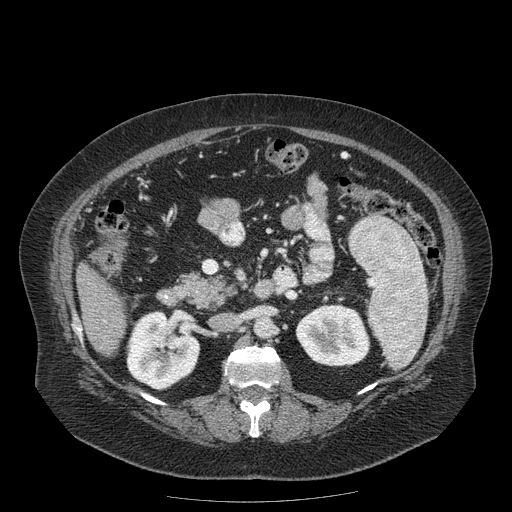
Contrast-enhanced abdominal CT (liver protocol), one axial slice. Slice 61 of 204 in the series (ordered by position). Reconstruction kernel STANDARD. 120 kVp. Soft-tissue window (W 400 / L 40 HU). 2.5 mm slice thickness. 512 × 512 image matrix, field of view 440 × 440 mm. Case-level facts recorded for this patient, not image findings: diagnosis: hepatocellular carcinoma (patient treated with transarterial chemoembolisation; whether this scan precedes or follows treatment is not stated here); TNM stage (as recorded): Stage-IIIB; Child-Pugh class: A; tumour differentiation: well differentiated; tumour nodularity: uninodular.
Structures marked on this image (semi-automatically segmented with operator editing):
- liver parenchyma outside the tumour (the mass and vessels are separate outlines, so this box may not span the whole liver): bounding box <76,262,126,355> (left, top, right, bottom; pixels)